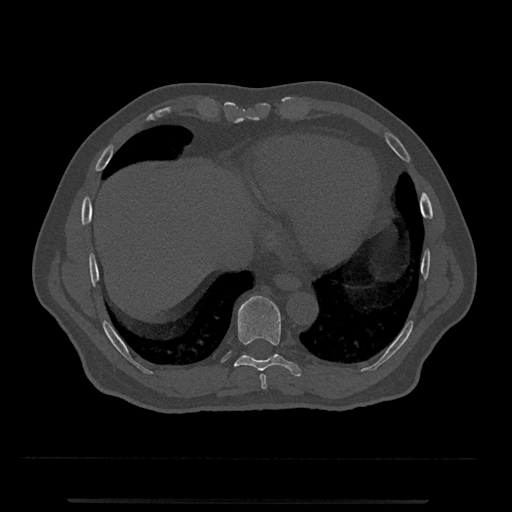
CT including the spine, one axial slice. Reconstruction kernel Br40s/3. 120 kVp. Bone window (W 1800 / L 400 HU). 0.5 mm slice thickness. 512 × 512 image matrix, field of view 419 × 419 mm. Male patient, age 63 years. From the clinical record (not read from this slice): primary cancer: prostate.
Outlined on this slice (semi-automatic segmentation, software-assisted and operator-edited):
- T8 vertebra: box from (x=260, y=374) to (x=267, y=390) px
- T9 vertebra: (x=234, y=296)–(x=303, y=377)